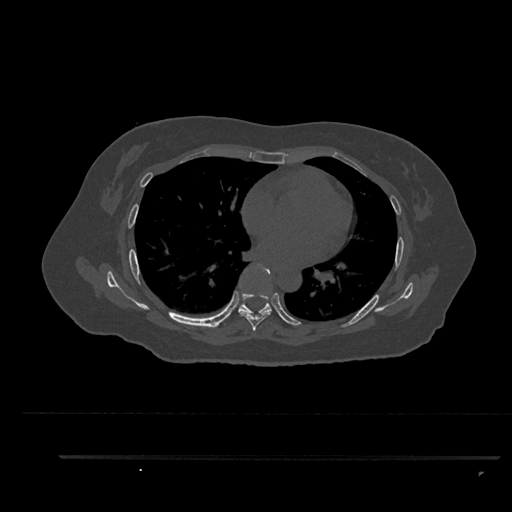
CT including the spine, one axial slice. Slice 535 of 797 in the series (ordered by position). Reconstruction kernel Br40s/3. 120 kVp. Bone window (W 1800 / L 400 HU). 512 × 512 image matrix, field of view 408 × 408 mm. Female patient, age 44 years. Case-level facts recorded for this patient, not image findings: primary cancer: renal; vertebrae with lytic lesions (as recorded): L1.
Annotated regions visible in this slice (semi-automatically segmented with operator editing):
- T6 vertebra: bounding box (x1, y1, x2, y2) in pixels: (240, 265, 271, 334)
- T7 vertebra: (238, 279, 272, 315)